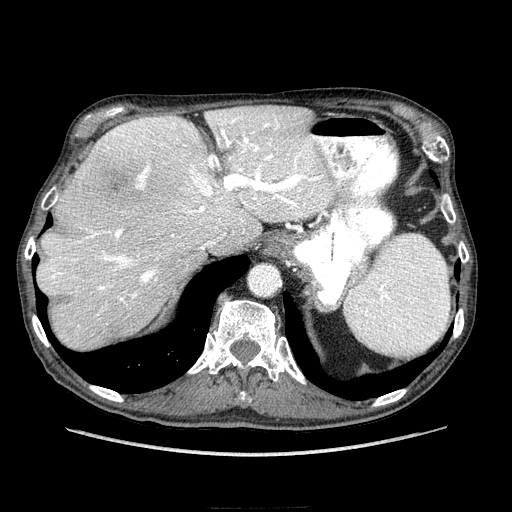
Contrast-enhanced abdominal CT (liver protocol), one axial slice. Position 171 of 218 along the scan axis. Soft-tissue window (W 400 / L 40 HU). 512 × 512 image matrix, field of view 380 × 380 mm. Case-level facts recorded for this patient, not image findings: diagnosis: hepatocellular carcinoma (patient treated with transarterial chemoembolisation; whether this scan precedes or follows treatment is not stated here); TNM stage (as recorded): Stage-IIIA; Child-Pugh class: A; tumour differentiation: well differentiated.
Annotated regions visible in this slice (semi-automatically segmented with operator editing):
- abdominal aorta: bounding box (x1, y1, x2, y2) in pixels: (250, 266, 280, 295)
- liver parenchyma outside the tumour (the mass and vessels are separate outlines, so this box may not span the whole liver): (38, 106, 336, 350)
- mass: (93, 166, 136, 207)
- liver vessels: (43, 114, 329, 316)